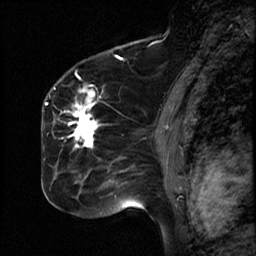
Breast MRI (dynamic contrast-enhanced), one sagittal slice. Position 32 of 50 along the scan axis. Dynamic contrast-enhanced study with each time point stored as its own series, time point 2 of 4 at this slice position (early post-contrast, ordered by acquisition time). 1.5 T. TE 4.2 ms, TR 18.5 ms. 256 × 256 image matrix. Female patient, age 44 years. Case-level facts recorded for this patient, not image findings: setting: breast cancer imaged before/during neoadjuvant chemotherapy; receptor status: HR-positive, HER2-negative.
Structures marked on this image (semi-automatic segmentation, software-assisted and operator-edited):
- analysis volume of interest (the breast-tissue region the enhancement analysis was run in; not a lesion): box from (x=59, y=80) to (x=114, y=206) px
- tumour enhancement mask (voxels above the 100 % enhancement threshold inside the analysis volume of interest): (x=67, y=101)–(x=99, y=148)